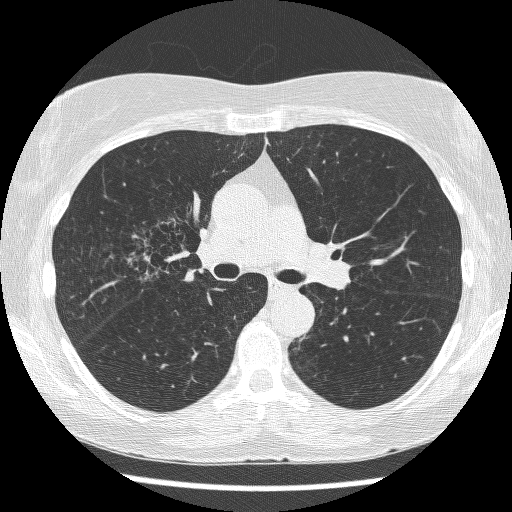
Low-dose screening chest CT, axial slice, baseline annual screen, lung window (W 1500 / L -600 HU), 1.25 mm slice thickness. Female, age 64 years at enrolment. Former smoker at enrolment.
Expert reader's lesion annotation, bounding box [x1, y1, x2, y2] px = [124, 218, 202, 283]. The screening reader recorded 3 non-calcified nodules or masses ≥4 mm on this exam (right upper lobe, right upper lobe, left lower lobe); which of them this box marks is not recorded. Lung cancer was diagnosed 735 days after this screen: adenocarcinoma, NOS, right upper lobe, right middle lobe, right hilum, stage IV (AJCC 6th edition), 85 mm at pathology.